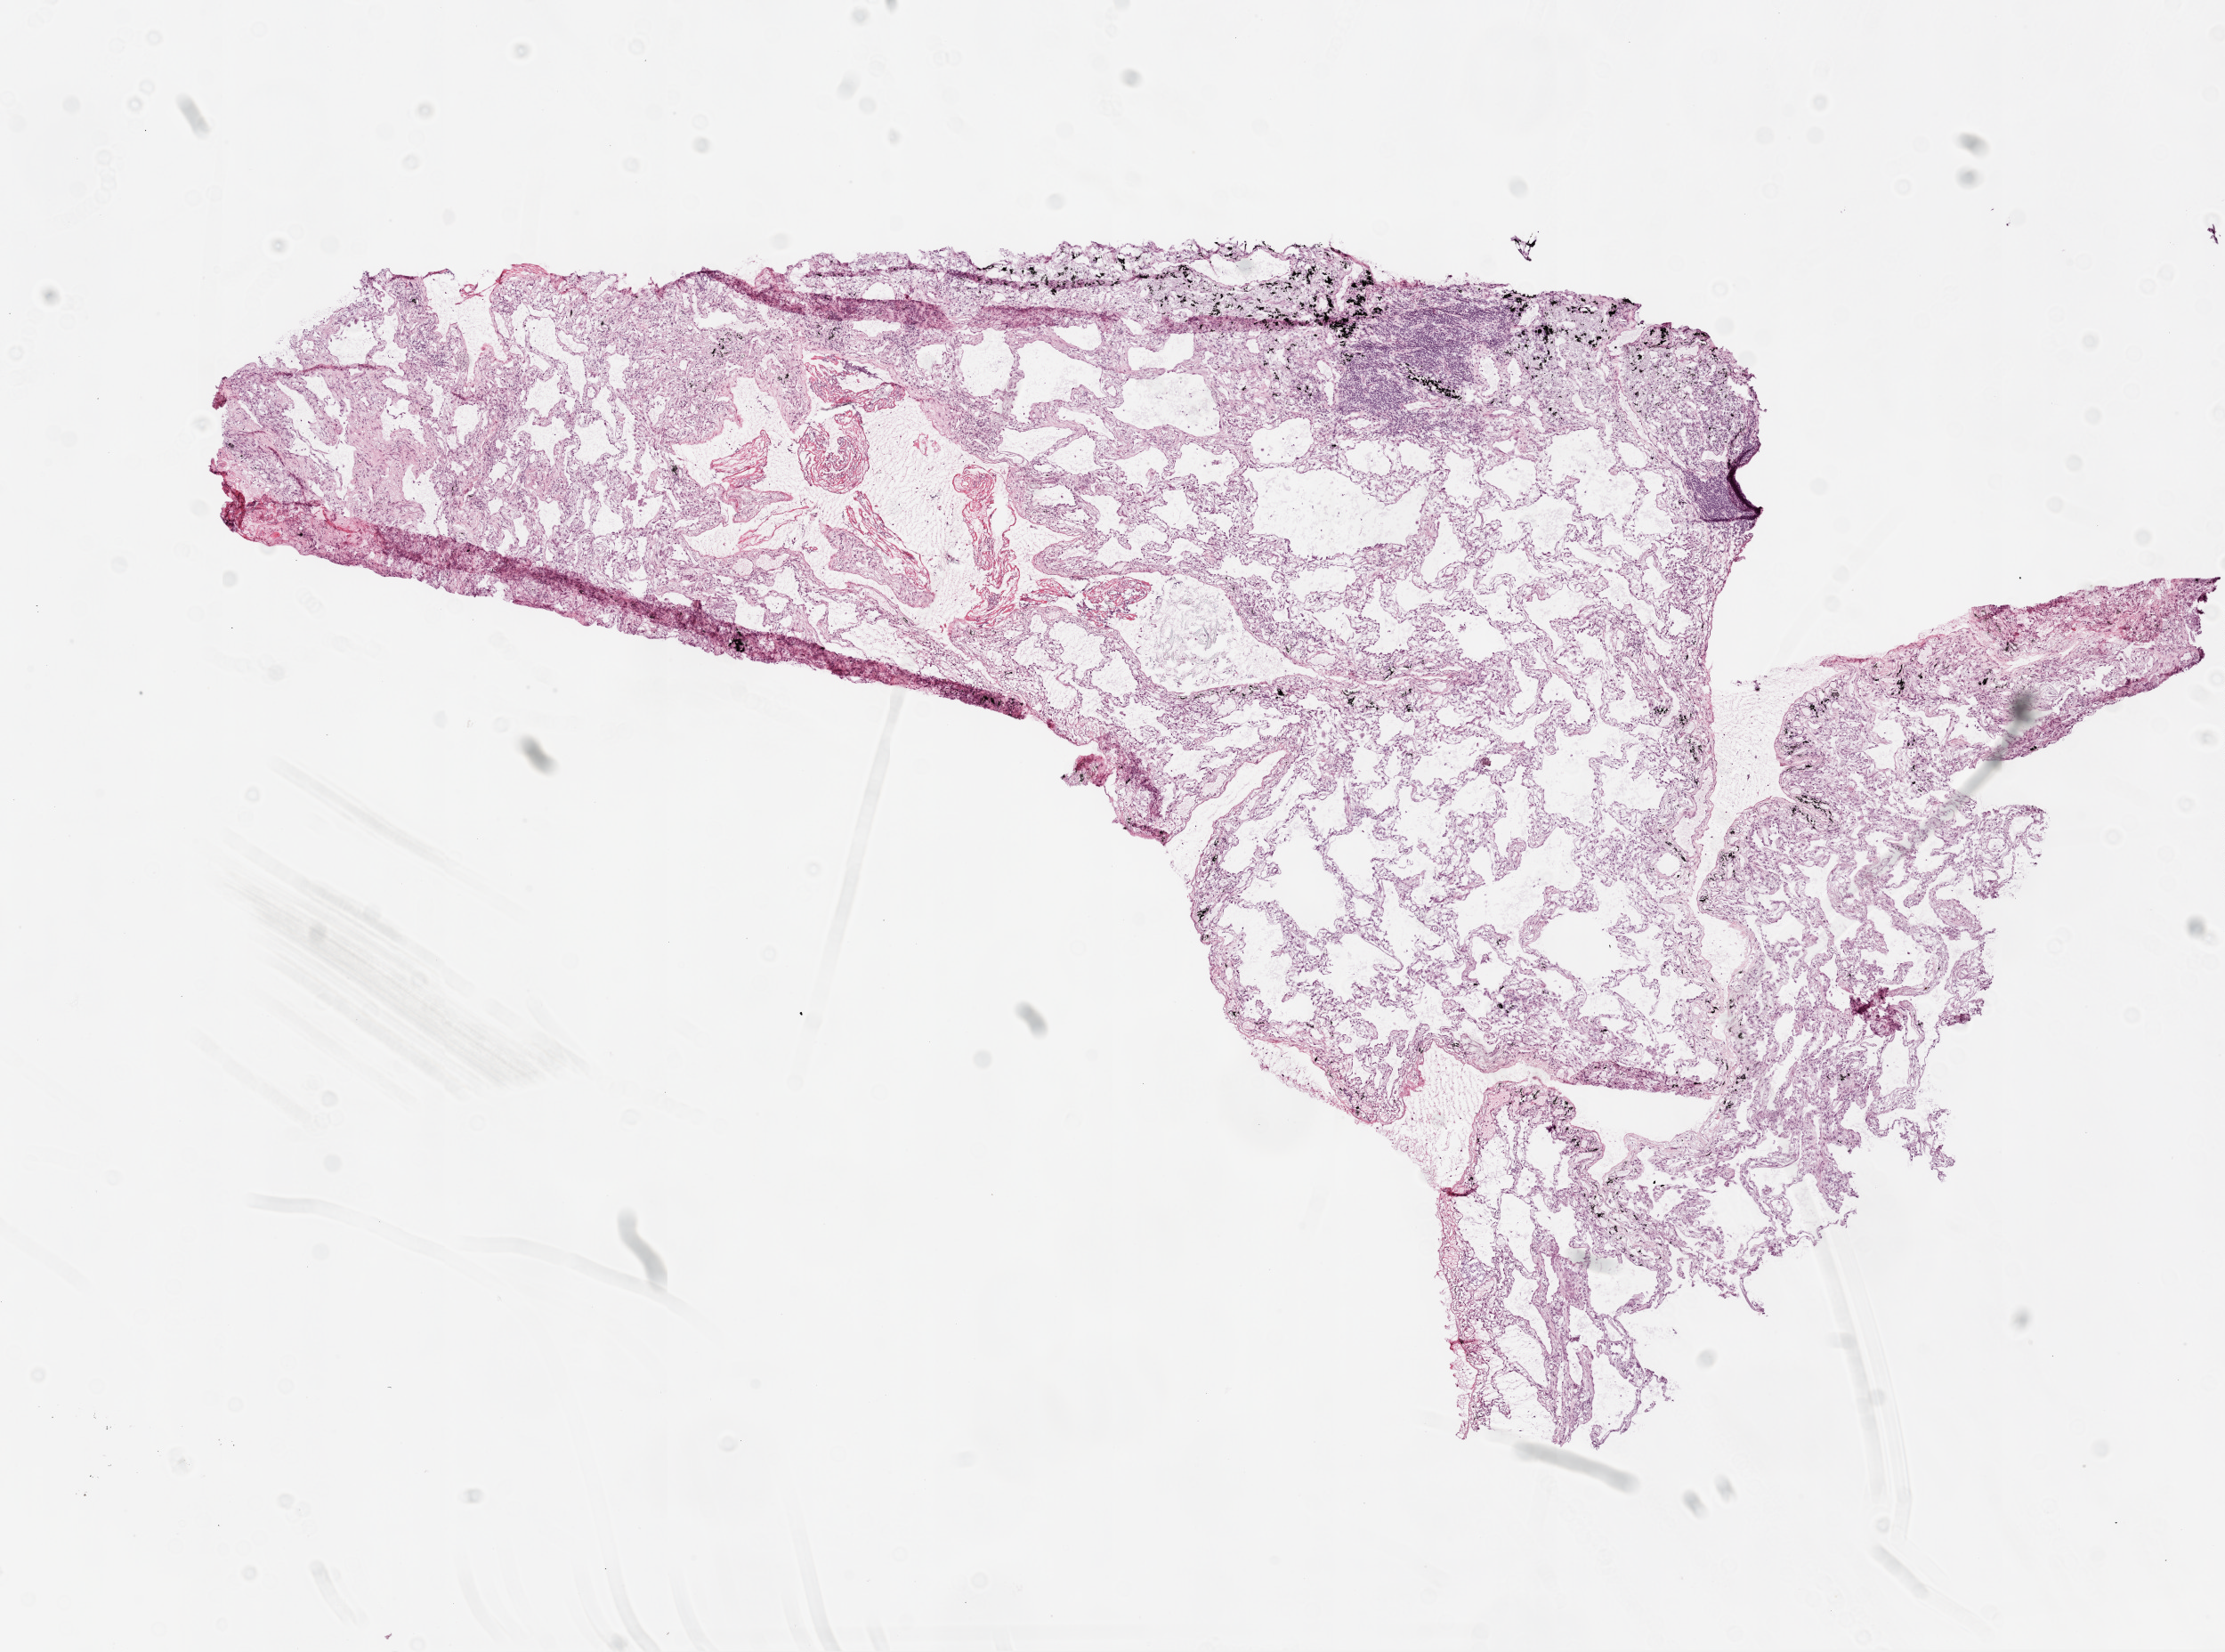
Digitized H&E tissue section (whole slide), shown as a low-resolution overview of the whole scanned area (about 10.0 x 7.4 mm, acquisition: 20x scan); frozen section; solid tissue normal (non-tumour tissue) sample from the lung. Female patient; age at initial diagnosis 76 years.
This section: solid tissue normal (non-tumour) sample from the same patient. Patient diagnosis: Squamous cell carcinoma, NOS (upper lobe, lung).